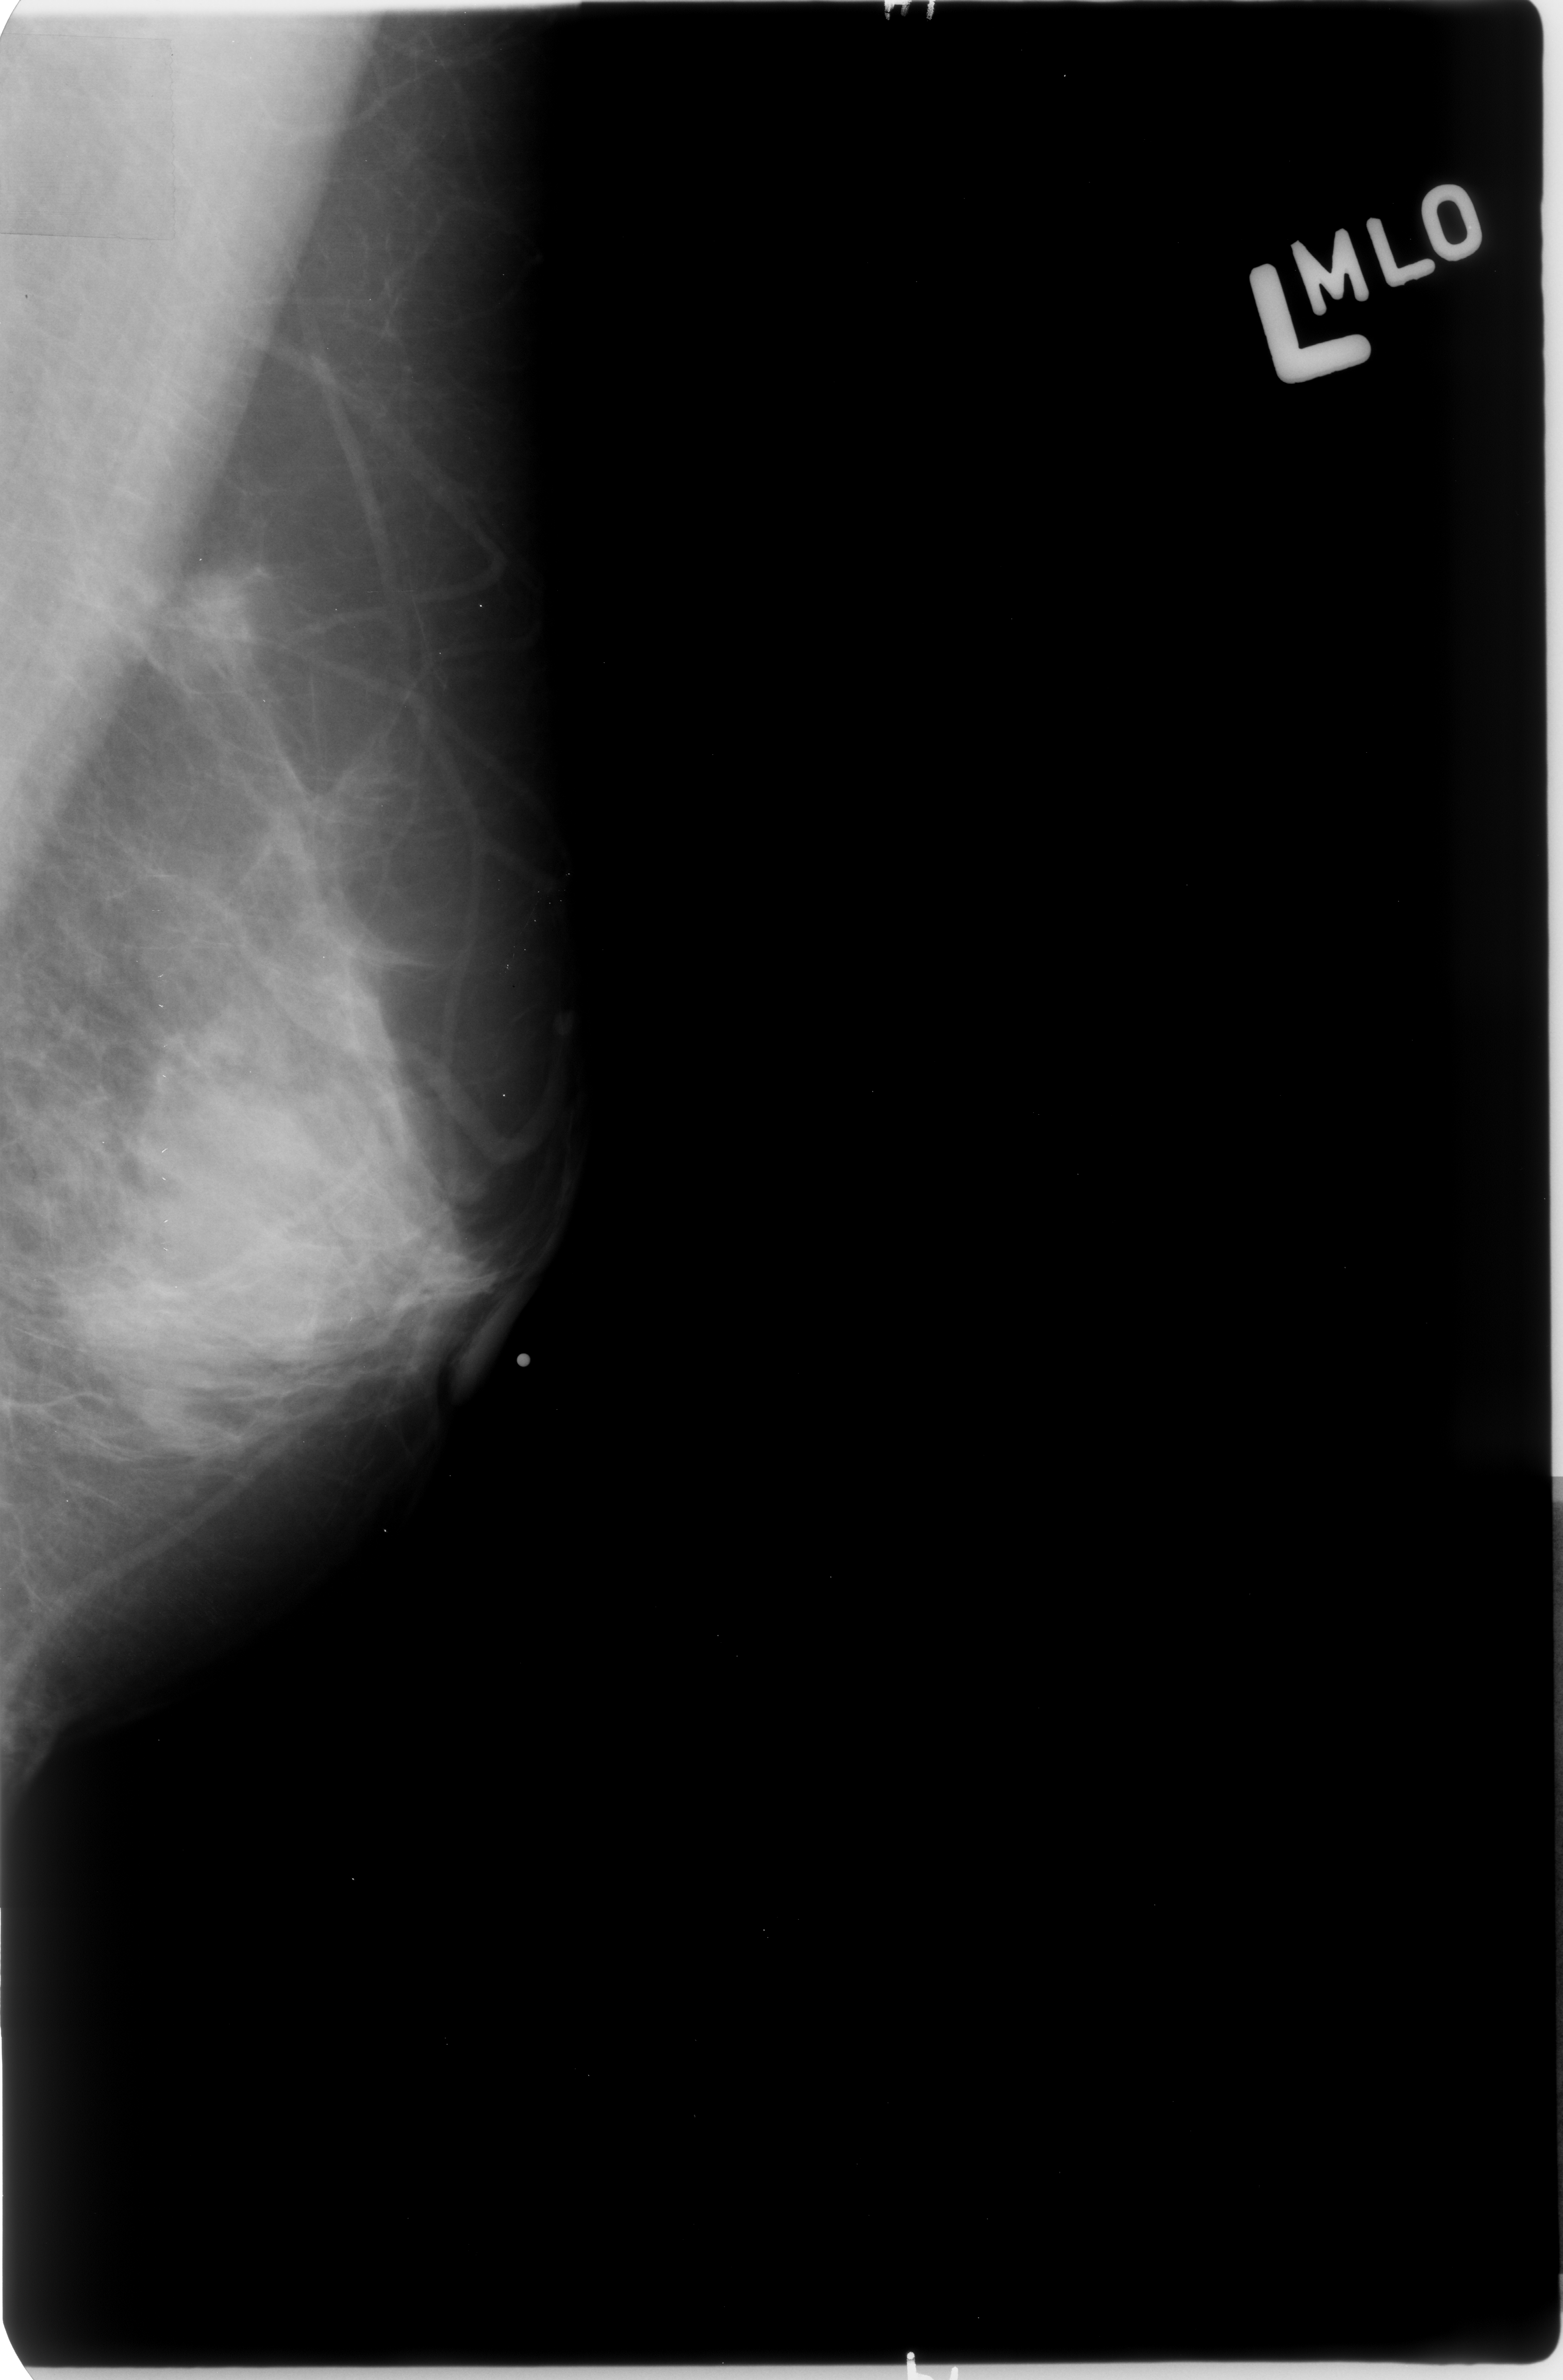
Digitized screen-film mammogram; left breast; MLO view; BI-RADS breast density category 3 (scale 1–4); 1563 × 2380 image matrix.
Marked abnormalities (boxes around the expert regions of interest):
- mass, shape irregular, margins ill defined / spiculated; BI-RADS assessment category 4; pathology result (as recorded, not read from the image): malignant: bounding box [x1, y1, x2, y2] px = [111, 567, 249, 654]